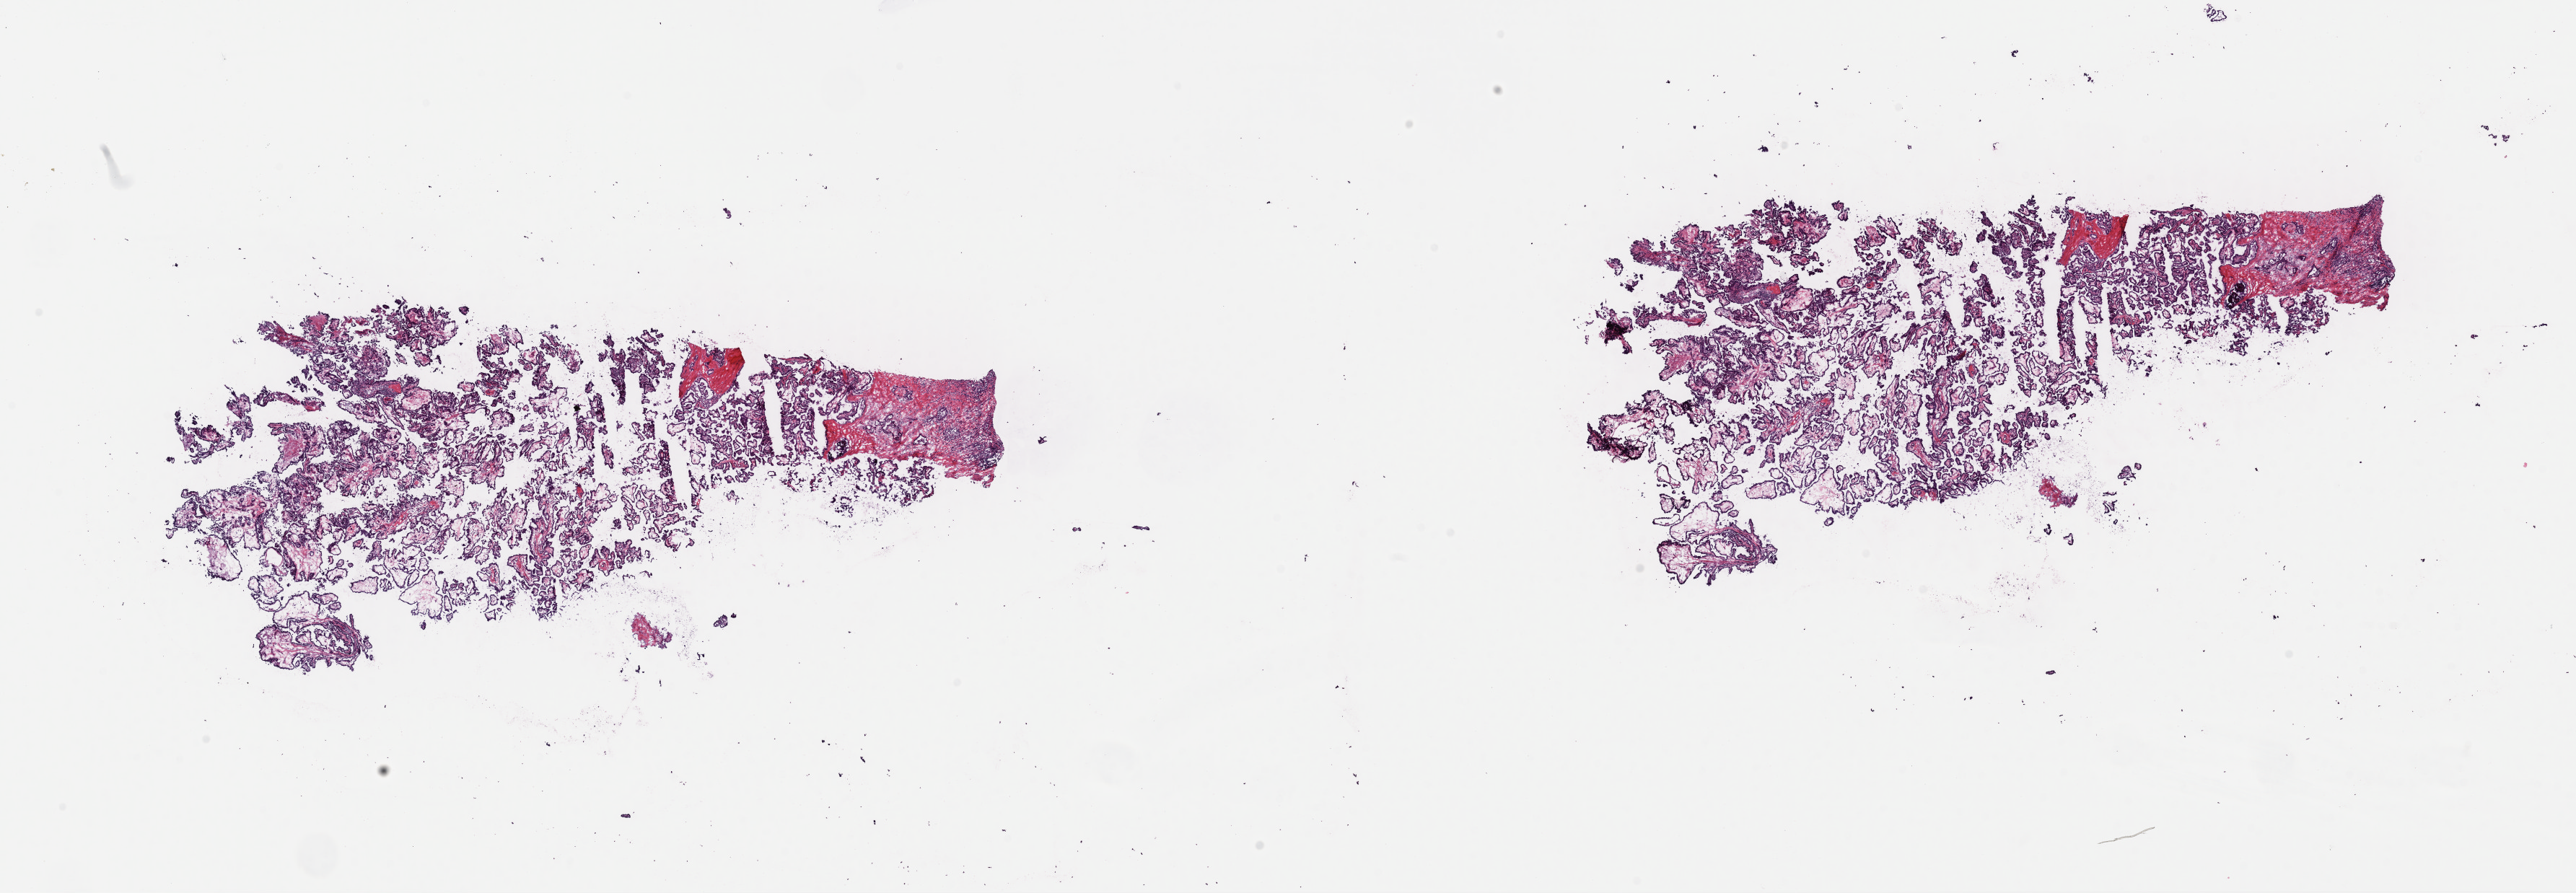
Whole-slide histology image, Hematoxylin and eosin (H&E) stained, shown as a low-resolution overview of the whole scanned area (about 28.2 x 9.8 mm). Frozen section from the top of the tissue portion. Sample: primary tumour, thyroid. Male, age 53 years at initial diagnosis. Slide review estimates, as recorded: tumour cells 85%, tumour nuclei 65%, normal cells 0%, stromal cells 15%, necrosis 0%. Infiltration values recorded for this section: lymphocyte infiltration 1%, monocyte infiltration 0%, neutrophil infiltration 0%.
Laterality: bilateral. TNM: T1b N1a M0. AJCC pathologic stage: III (7th edition). Pathologic diagnosis: Papillary adenocarcinoma, NOS (thyroid gland).